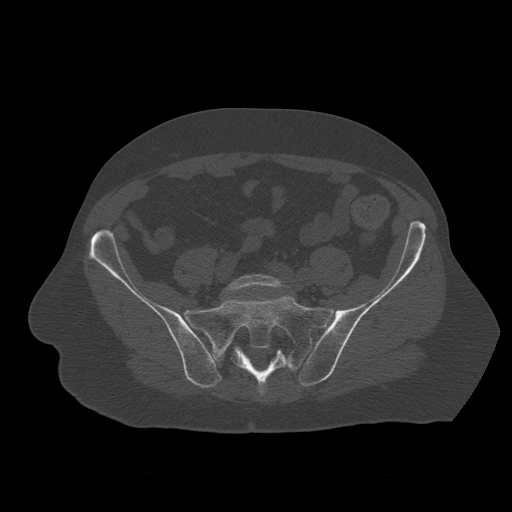
CT including the spine, one axial slice. Position 235 of 450 along the scan axis. Bone window (W 1800 / L 400 HU). 512 × 512 image matrix, field of view 405 × 405 mm. Patient age 75 years. Case-level facts recorded for this patient, not image findings: primary cancer: prostate.
Structures marked on this image (semi-automatic segmentation, software-assisted and operator-edited):
- L5 vertebra: bounding box (x1, y1, x2, y2) in pixels: (225, 274, 292, 293)